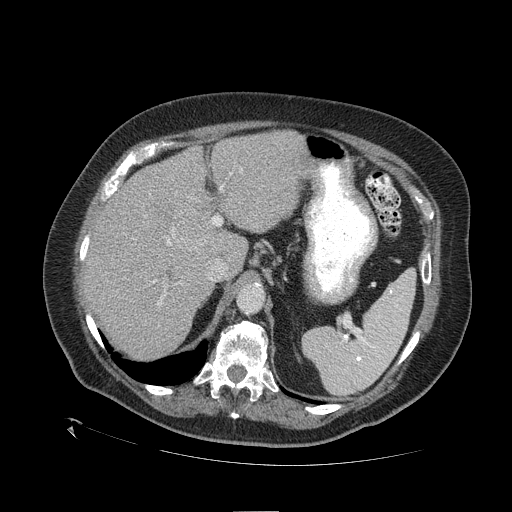
Contrast-enhanced abdominal CT (liver protocol), one axial slice; reconstruction kernel STANDARD; 120 kVp; one of 2 acquisitions stored at this slice position; soft-tissue window (W 400 / L 40 HU); 2.5 mm slice thickness; 512 × 512 image matrix, field of view 460 × 460 mm. Case-level facts recorded for this patient, not image findings: diagnosis: hepatocellular carcinoma (patient treated with transarterial chemoembolisation; whether this scan precedes or follows treatment is not stated here); TNM stage (as recorded): Stage-I; Child-Pugh class: A; tumour differentiation: no biopsy; tumour nodularity: uninodular.
Annotated regions visible in this slice (semi-automatically segmented with operator editing):
- liver parenchyma outside the tumour (the mass and vessels are separate outlines, so this box may not span the whole liver): bounding box [x1, y1, x2, y2] px = [82, 130, 310, 358]
- mass: [173, 211, 209, 250]
- liver vessels: [154, 172, 232, 306]